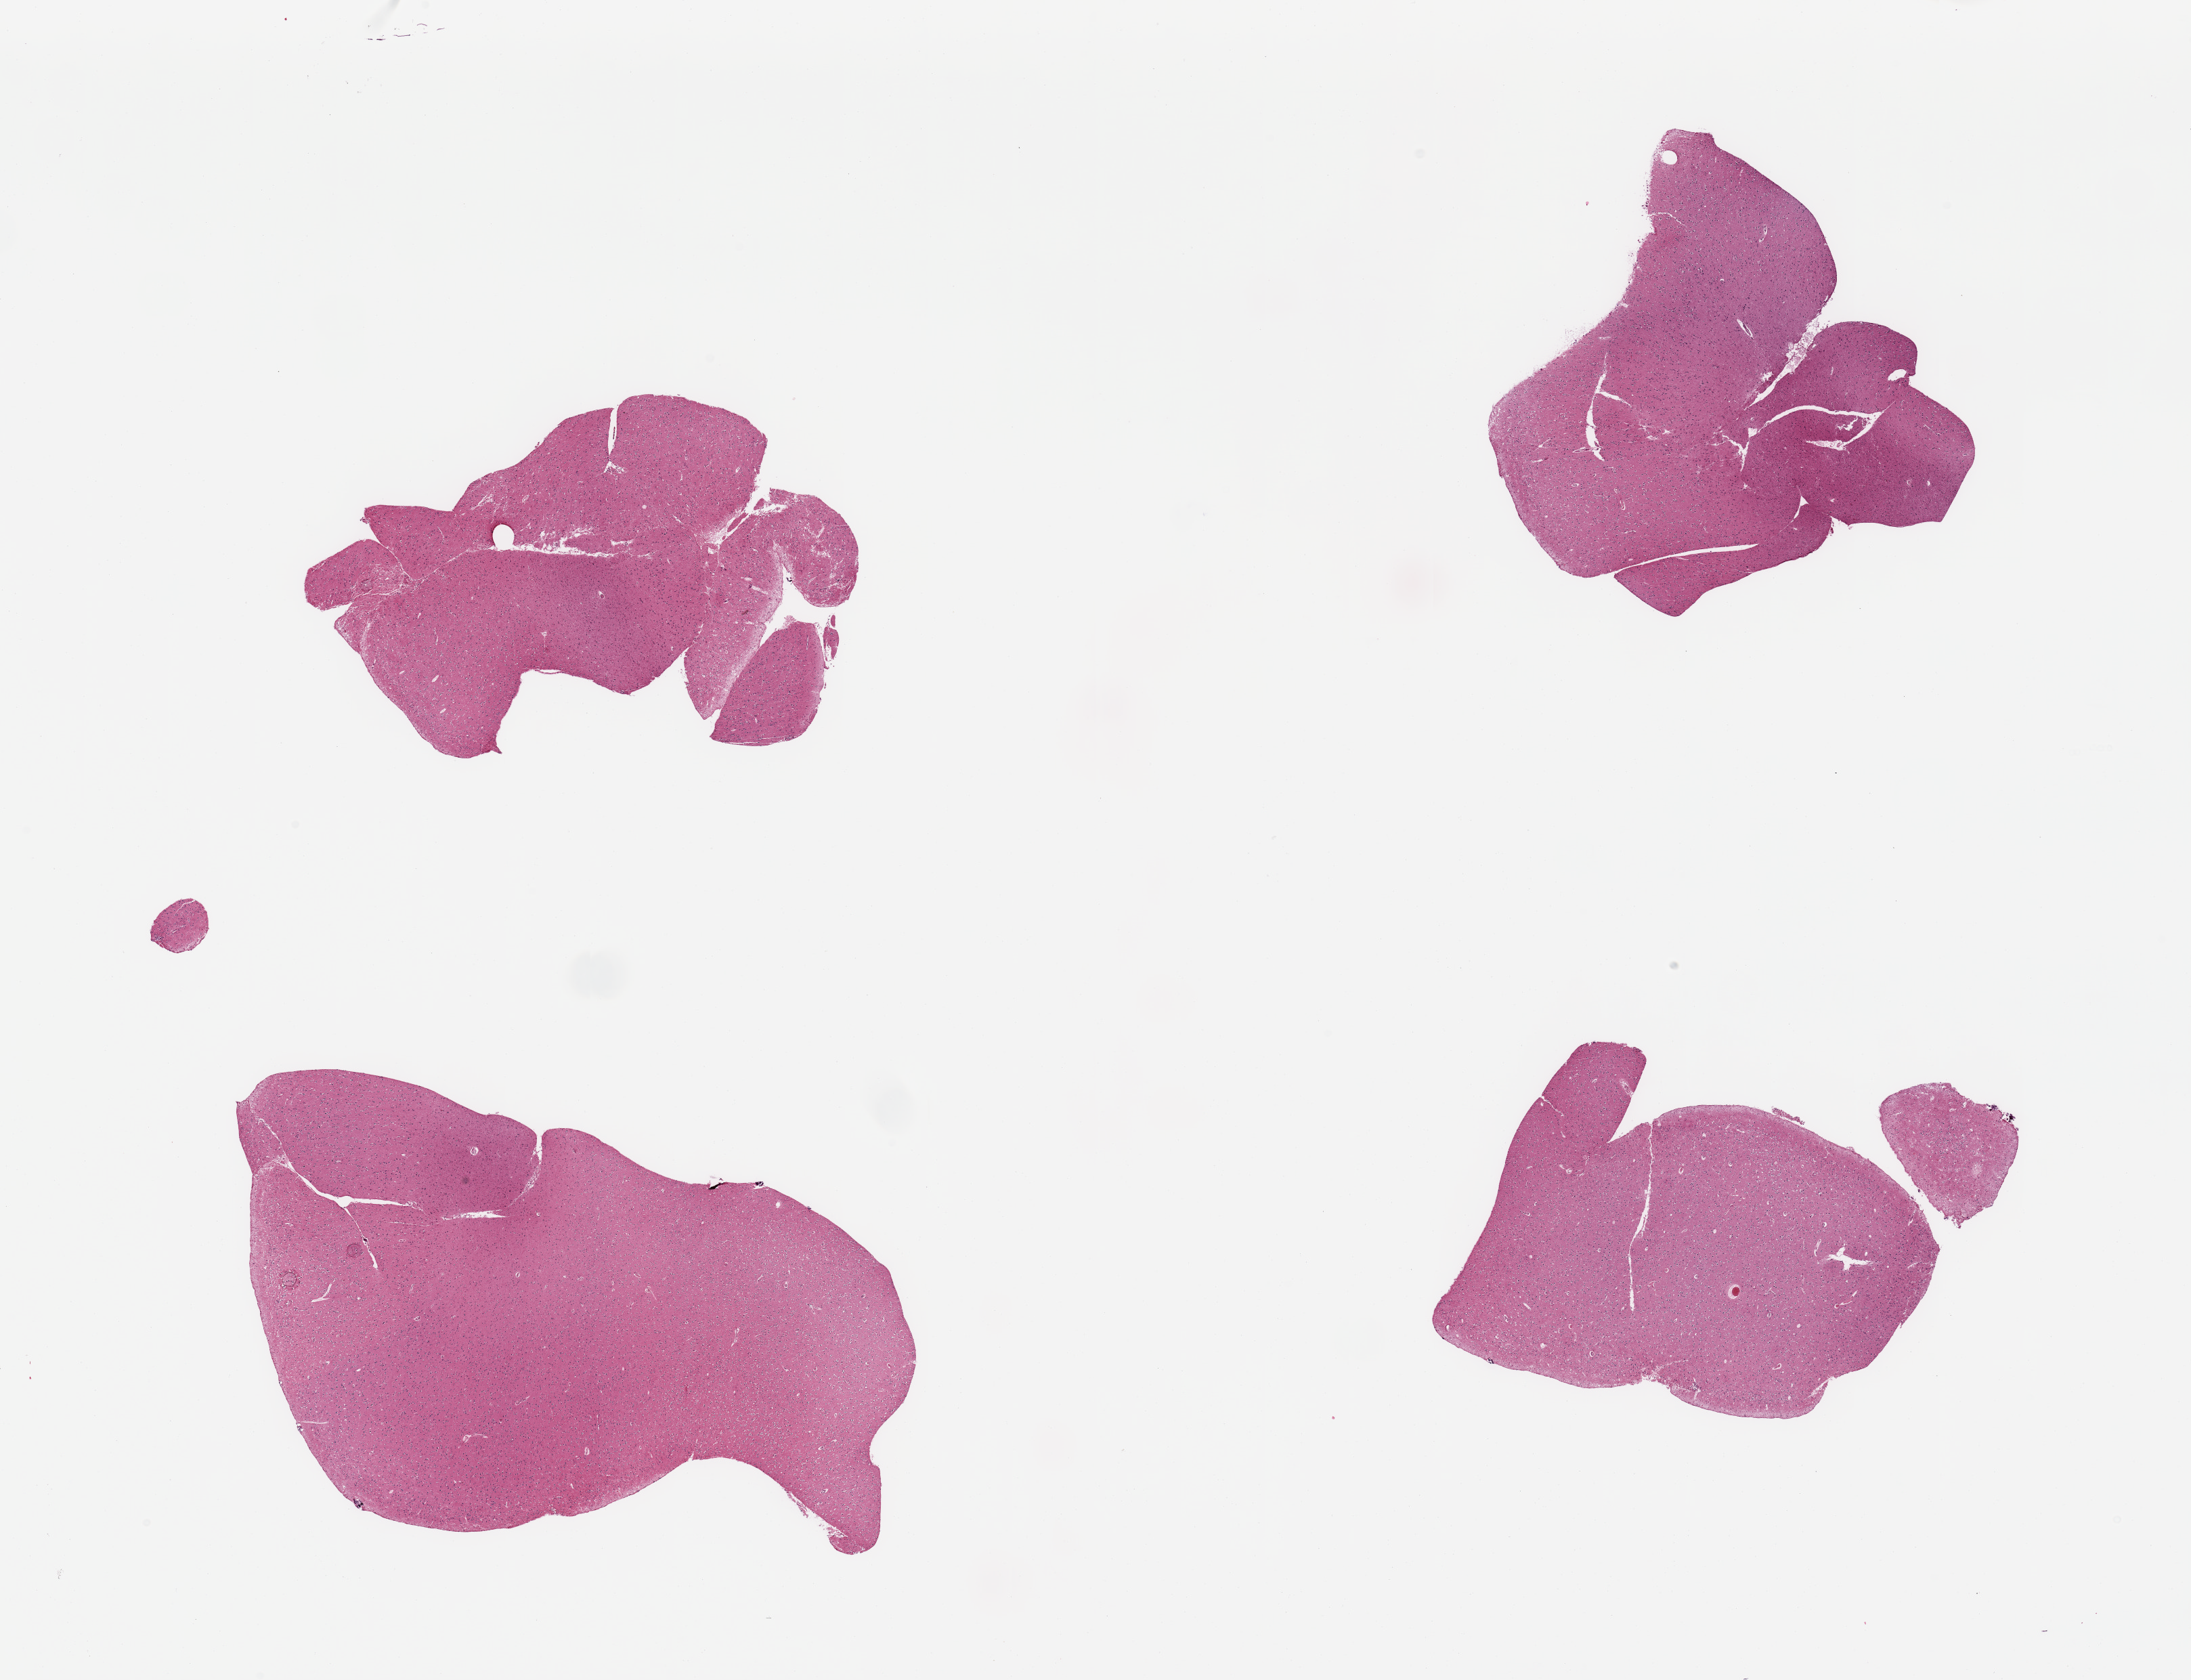
Digitized haematoxylin and eosin-stained section, shown as a low-resolution overview of the whole scanned area (about 25.6 x 19.6 mm, slide scanned at 20x). PAXgene-fixed paraffin-embedded (PFPE) section. Sampled site (target tissue): cerebral cortex. Donor tissue sample. Donor: male.
• review note (as recorded): 4 pieces